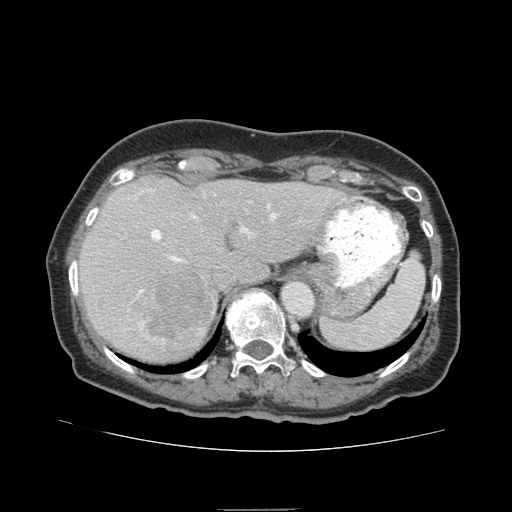
Contrast-enhanced abdominal CT (liver protocol), one axial slice. Position 60 of 95 along the scan axis. Reconstruction kernel STANDARD. Soft-tissue window (W 400 / L 40 HU). 2.5 mm slice thickness. 512 × 512 image matrix, field of view 360 × 360 mm. From the clinical record (not read from this slice): diagnosis: hepatocellular carcinoma (patient treated with transarterial chemoembolisation; whether this scan precedes or follows treatment is not stated here); TNM stage (as recorded): Stage-IVA; Child-Pugh class: B; tumour nodularity: uninodular.
Structures marked on this image (semi-automatic segmentation, software-assisted and operator-edited):
- liver parenchyma outside the tumour (the mass and vessels are separate outlines, so this box may not span the whole liver): bounding box (x1, y1, x2, y2) in pixels: (78, 176, 348, 362)
- mass: (132, 270, 217, 357)
- liver vessels: (139, 204, 276, 293)